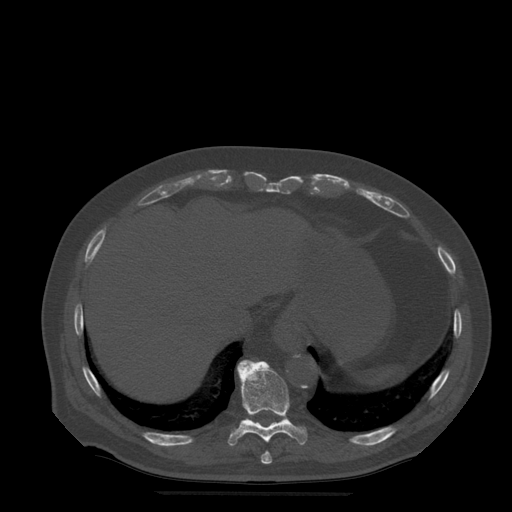
CT including the spine, one axial slice. Position 266 of 522 along the scan axis. Bone window (W 1800 / L 400 HU). 512 × 512 image matrix, field of view 420 × 420 mm. Patient age 72 years. From the clinical record (not read from this slice): primary cancer: prostate.
Annotated regions visible in this slice (semi-automatically segmented with operator editing):
- T10 vertebra: bounding box <228,361,308,446> (left, top, right, bottom; pixels)
- T11 vertebra: <246,360,251,362>
- T9 vertebra: <261,451,272,465>